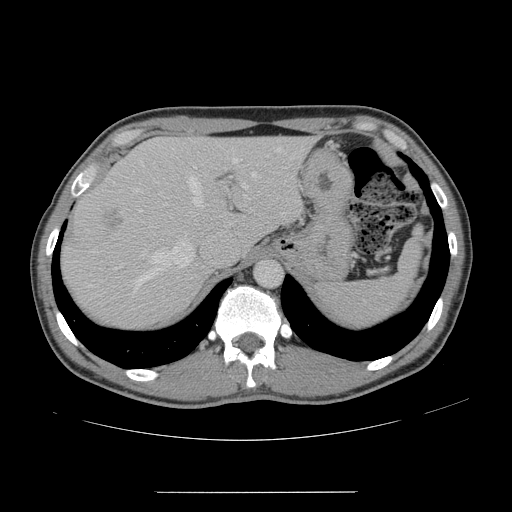
Contrast-enhanced abdominal CT, one axial slice; position 115 of 178 along the scan axis; 120 kVp; intravenous contrast given; soft-tissue window (W 400 / L 40 HU); 2.5 mm slice thickness; 512 × 512 image matrix, field of view 401 × 401 mm. Male patient, age 53 years. Case-level facts recorded for this patient, not image findings: diagnosis: colorectal cancer liver metastases, imaged before liver resection; multiple liver metastases: yes; largest metastasis: 2.4 cm.
Structures marked on this image (outlined manually by an expert reader):
- hepatic veins: bounding box <134,147,281,291> (left, top, right, bottom; pixels)
- liver: <63,137,310,327>
- planned liver remnant (the part of the liver to remain after resection): <147,136,310,247>
- portal vein (with intrahepatic branches): <139,168,248,212>
- liver metastasis: <103,209,123,230>